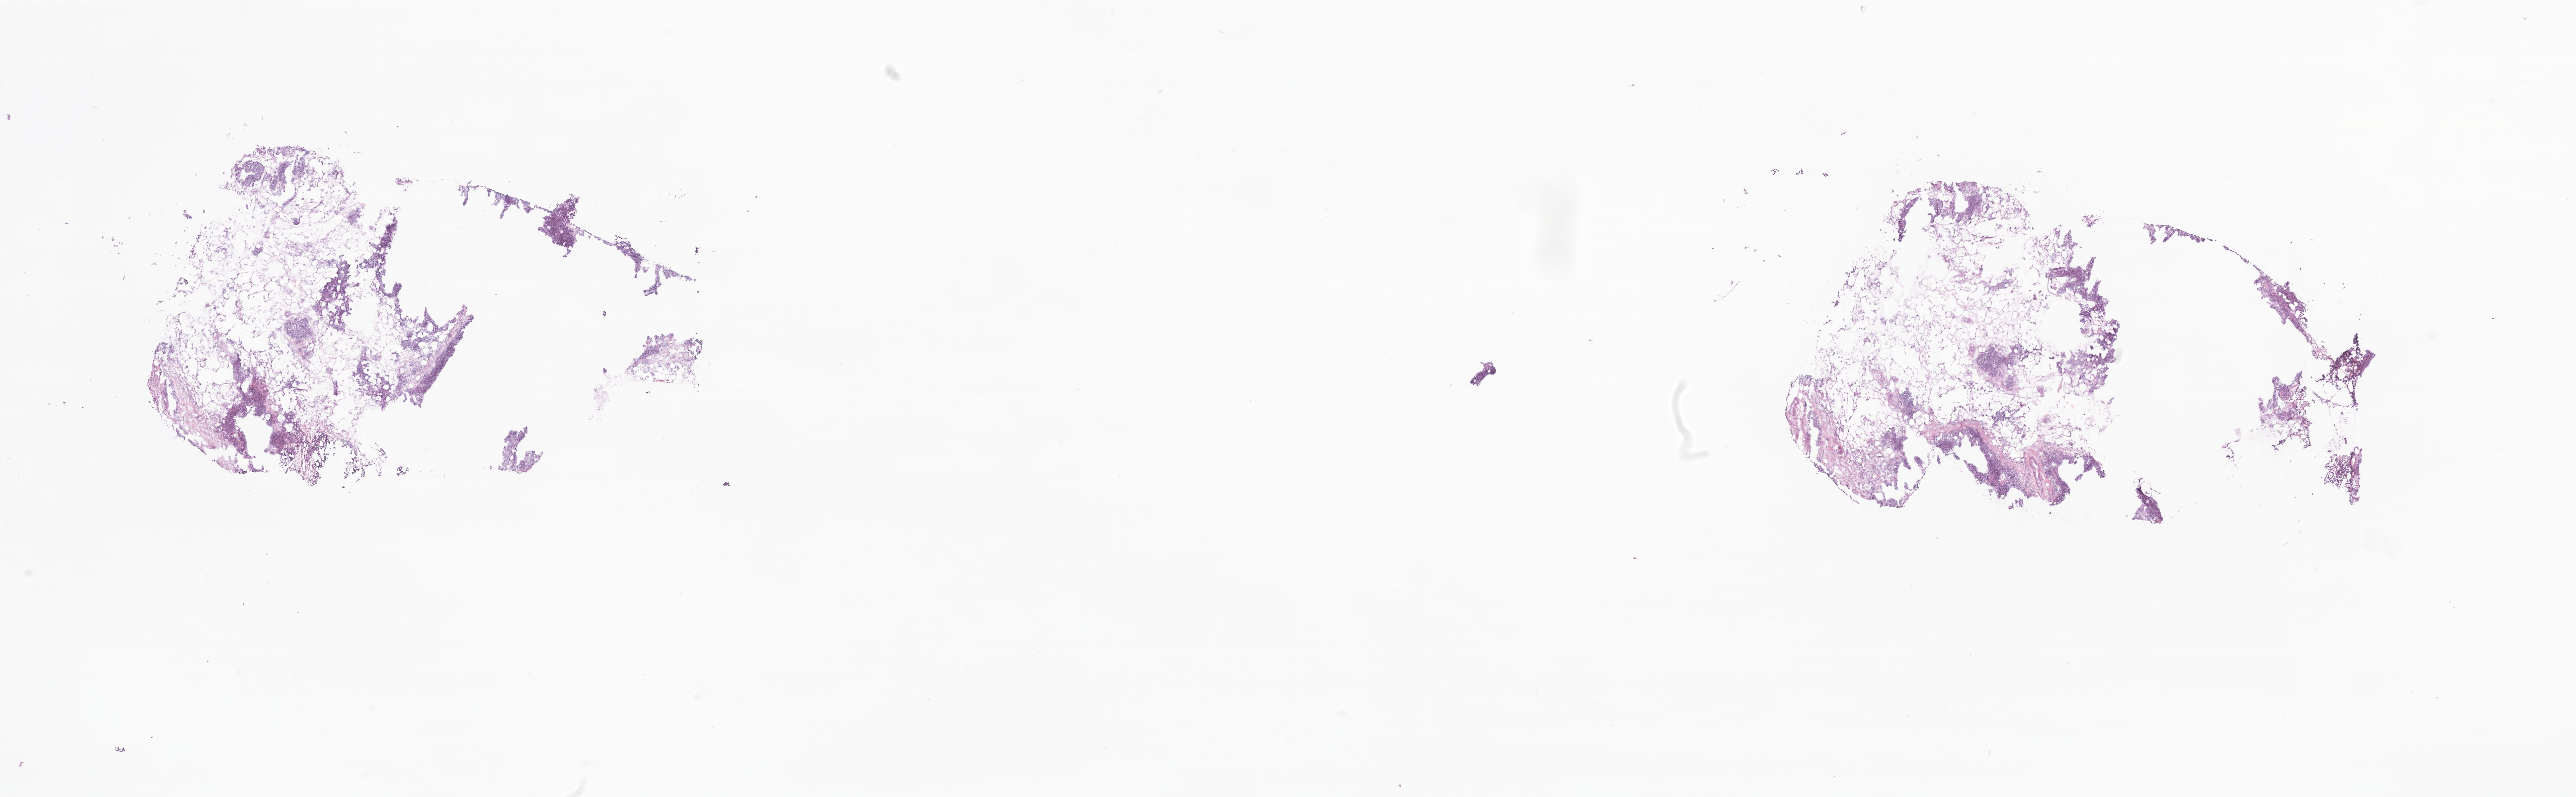
Whole-slide image, hematoxylin and eosin (H&E) stain — low-resolution overview of the scanned area, about 32.4 x 10.0 mm; cryosection; primary tumor; site: breast (right). Female patient; age at initial diagnosis 86 years. Pathologist review of this section (percent, as recorded): tumor cells 25%, tumor nuclei 25%, stromal cells 10%, necrosis 0%, normal cells 65%. Inflammatory infiltration, as recorded: lymphocyte infiltration 10%, monocyte infiltration 5%, neutrophil infiltration 10%.
- histologic diagnosis: Infiltrating duct carcinoma, NOS